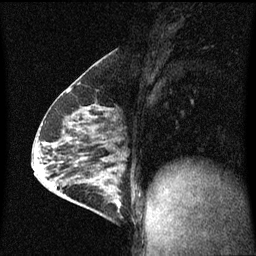
Breast MRI (dynamic contrast-enhanced), one sagittal slice; position 31 of 60 along the scan axis; dynamic contrast-enhanced series, image 2 of 3 at this slice position (ordered by acquisition); 1.5 T; TE 4.2 ms, TR 8 ms; 2 mm slice thickness; 256 × 256 image matrix, field of view 200 × 200 mm. Patient: female, 64 years.
Outlined on this slice (semi-automatically segmented with operator editing):
- analysis volume of interest (the breast-tissue region the enhancement analysis was run in; not a lesion): box from (x=87, y=176) to (x=123, y=217) px
- tumour enhancement mask (voxels above the 70 % enhancement threshold inside the analysis volume of interest): (x=99, y=176)–(x=121, y=209)